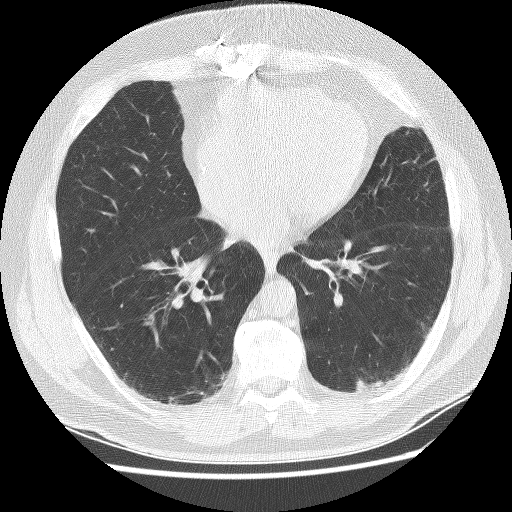
Axial slice from a low-dose chest CT screening exam. Baseline screening round. Lung window (W 1500 / L -600 HU). 120 kVp. Slice 135 of 236 in the series. Male, age 65 years at enrolment. Former smoker at enrolment.
- Expert-annotated lung lesion, bounding box (x1, y1, x2, y2) in pixels: (352, 370, 392, 405).
- Screening reader's record for this exam: no non-calcified nodule ≥4 mm recorded.
- Lung cancer was diagnosed 523 days after this screen (after the second annual screen): squamous cell carcinoma, NOS, left lower lobe, moderately differentiated (G2), stage IA (AJCC 6th edition), 20 mm at pathology.